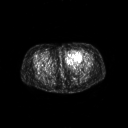
FDG PET of an extremity soft-tissue mass (from a PET/CT study), one axial slice. 3.27 mm slice thickness. 128 × 128 image matrix, field of view 700 × 700 mm. Patient: female, 47 years. From the clinical record (not read from this slice): histological type: myxofibrosarcoma; grade: intermediate; site of the primary tumour: left thigh.
Outlined on this slice (expert contour drawn on MRI and transferred to this co-registered scan by the dataset authors):
- gross tumour volume including surrounding oedema: bounding box (x1, y1, x2, y2) in pixels: (65, 51, 83, 66)
- gross tumour volume (mass): (66, 51, 82, 63)